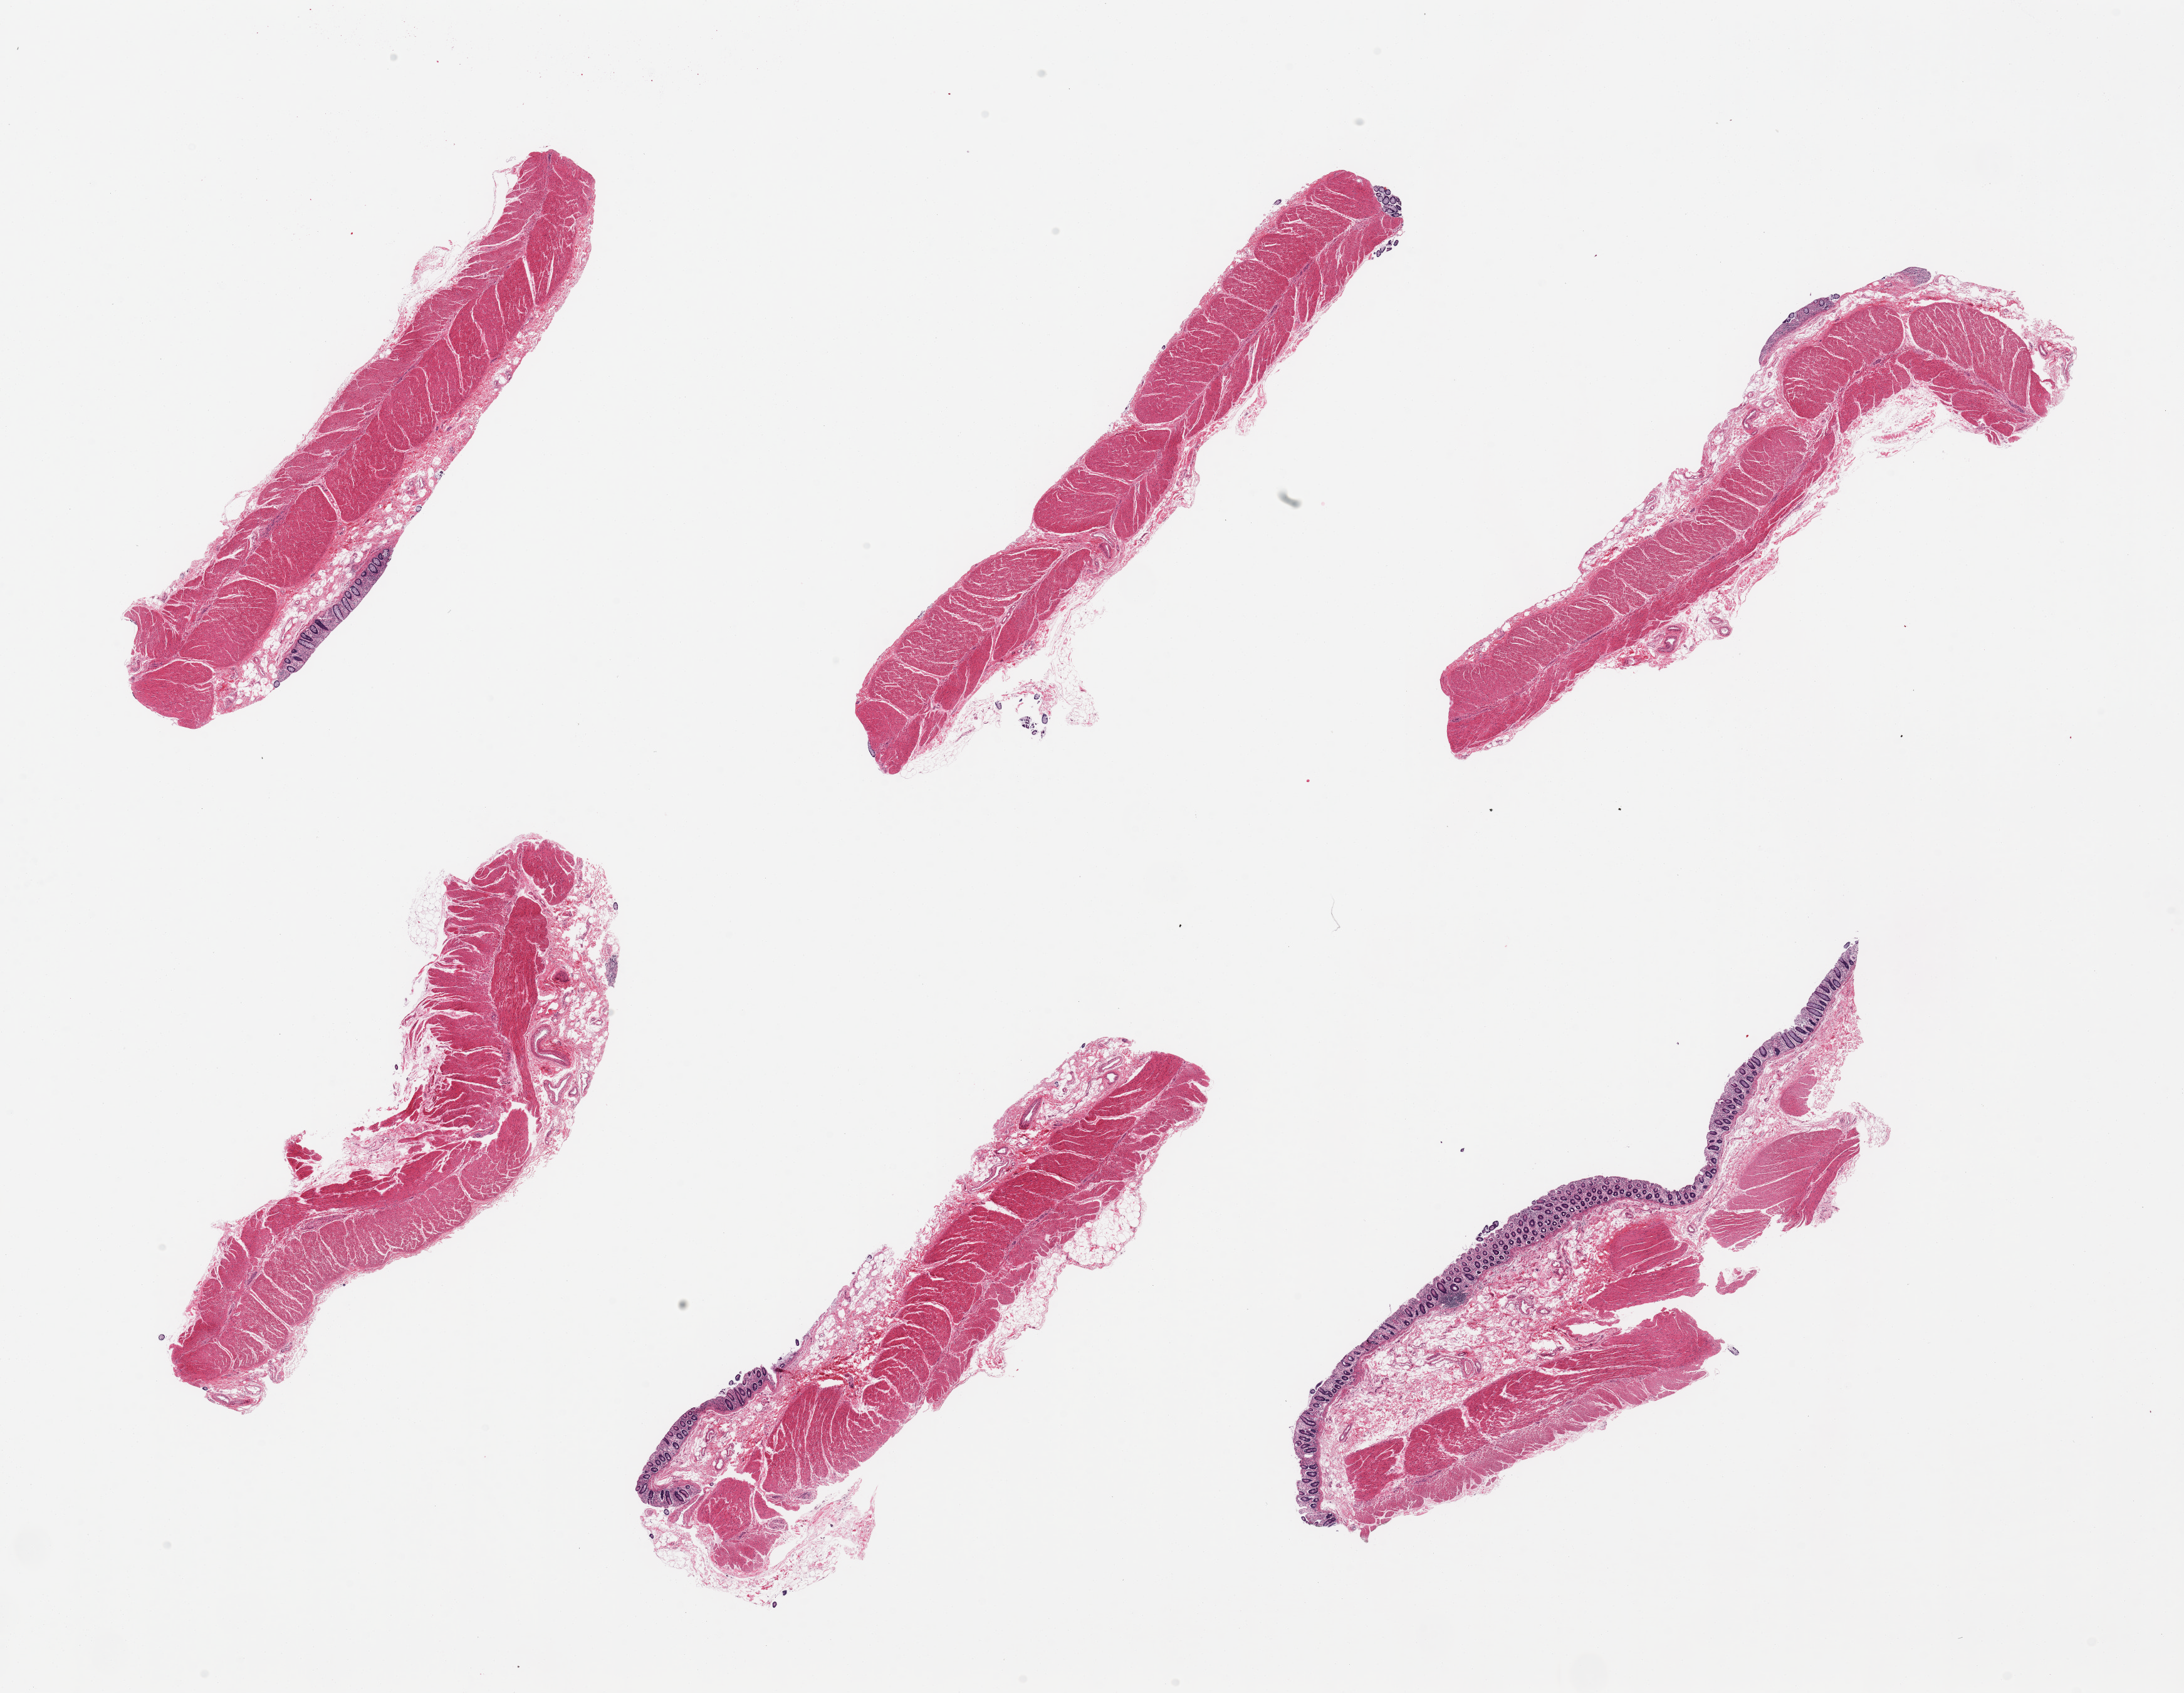
Haematoxylin and eosin whole-slide image, brightfield, low-resolution overview of the scanned area, about 27.6 x 21.4 mm; PAXgene-fixed, paraffin-embedded tissue; target tissue: sigmoid colon; tissue donor sample. Donor sex: female.
• review note (as recorded): 6 pieces; target muscularis, several pieces include strips of residual mucosa